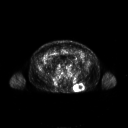
FDG PET of an extremity soft-tissue mass (from a PET/CT study), one axial slice; position 91 of 267 along the scan axis; 3.27 mm slice thickness; 128 × 128 image matrix, field of view 700 × 700 mm. Male patient, age 61 years. From the clinical record (not read from this slice): histological type: pleiomorphic leiomyosarcoma; grade: high; site of the primary tumour: left buttock.
Structures marked on this image (expert contour drawn on MRI and transferred to this co-registered scan by the dataset authors):
- gross tumour volume including surrounding oedema: box from (x=74, y=83) to (x=84, y=92) px
- gross tumour volume (mass): (x=74, y=84)–(x=84, y=92)